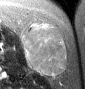
MRI of an extremity soft-tissue mass, one axial slice. Slice 19 of 46 in the series (ordered by position). T2-weighted fat-saturated. MR volume resampled by the dataset authors to the PET/CT grid (not the native acquisition matrix). 85 × 89 image matrix. Female patient. Case-level facts recorded for this patient, not image findings: histological type: leiomyosarcoma; grade: intermediate; site of the primary tumour: parascapusular.
Annotated regions visible in this slice (expert contour drawn on MRI and transferred to this co-registered scan by the dataset authors):
- gross tumour volume including surrounding oedema: bounding box <22,23,67,76> (left, top, right, bottom; pixels)
- gross tumour volume (mass): <22,23,67,76>